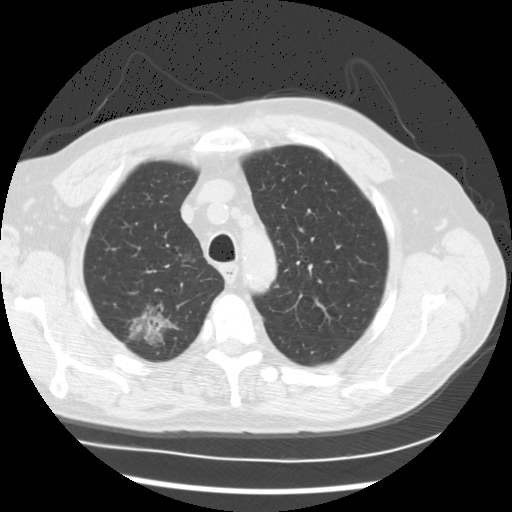
Low-dose screening chest CT, axial slice; first (baseline) screen; lung window (W 1500 / L -600 HU); 2.5 mm slice thickness; standard (soft-tissue) reconstruction kernel (STANDARD); 120 kVp; 512 × 512 image matrix. Male participant, aged 68 years at enrolment. Current smoker at enrolment.
Expert-annotated lung lesion, bounding box (x1, y1, x2, y2) in pixels: (114, 291, 188, 362). The screening reader recorded 3 non-calcified nodules or masses ≥4 mm on this exam (right upper lobe, right upper lobe, right lower lobe); which of them this box marks is not recorded. Lung cancer was diagnosed 90 days after this screen: adenocarcinoma, NOS, right upper lobe, right lower lobe, well differentiated (G1), stage IV (AJCC 6th edition), 35 mm at pathology.